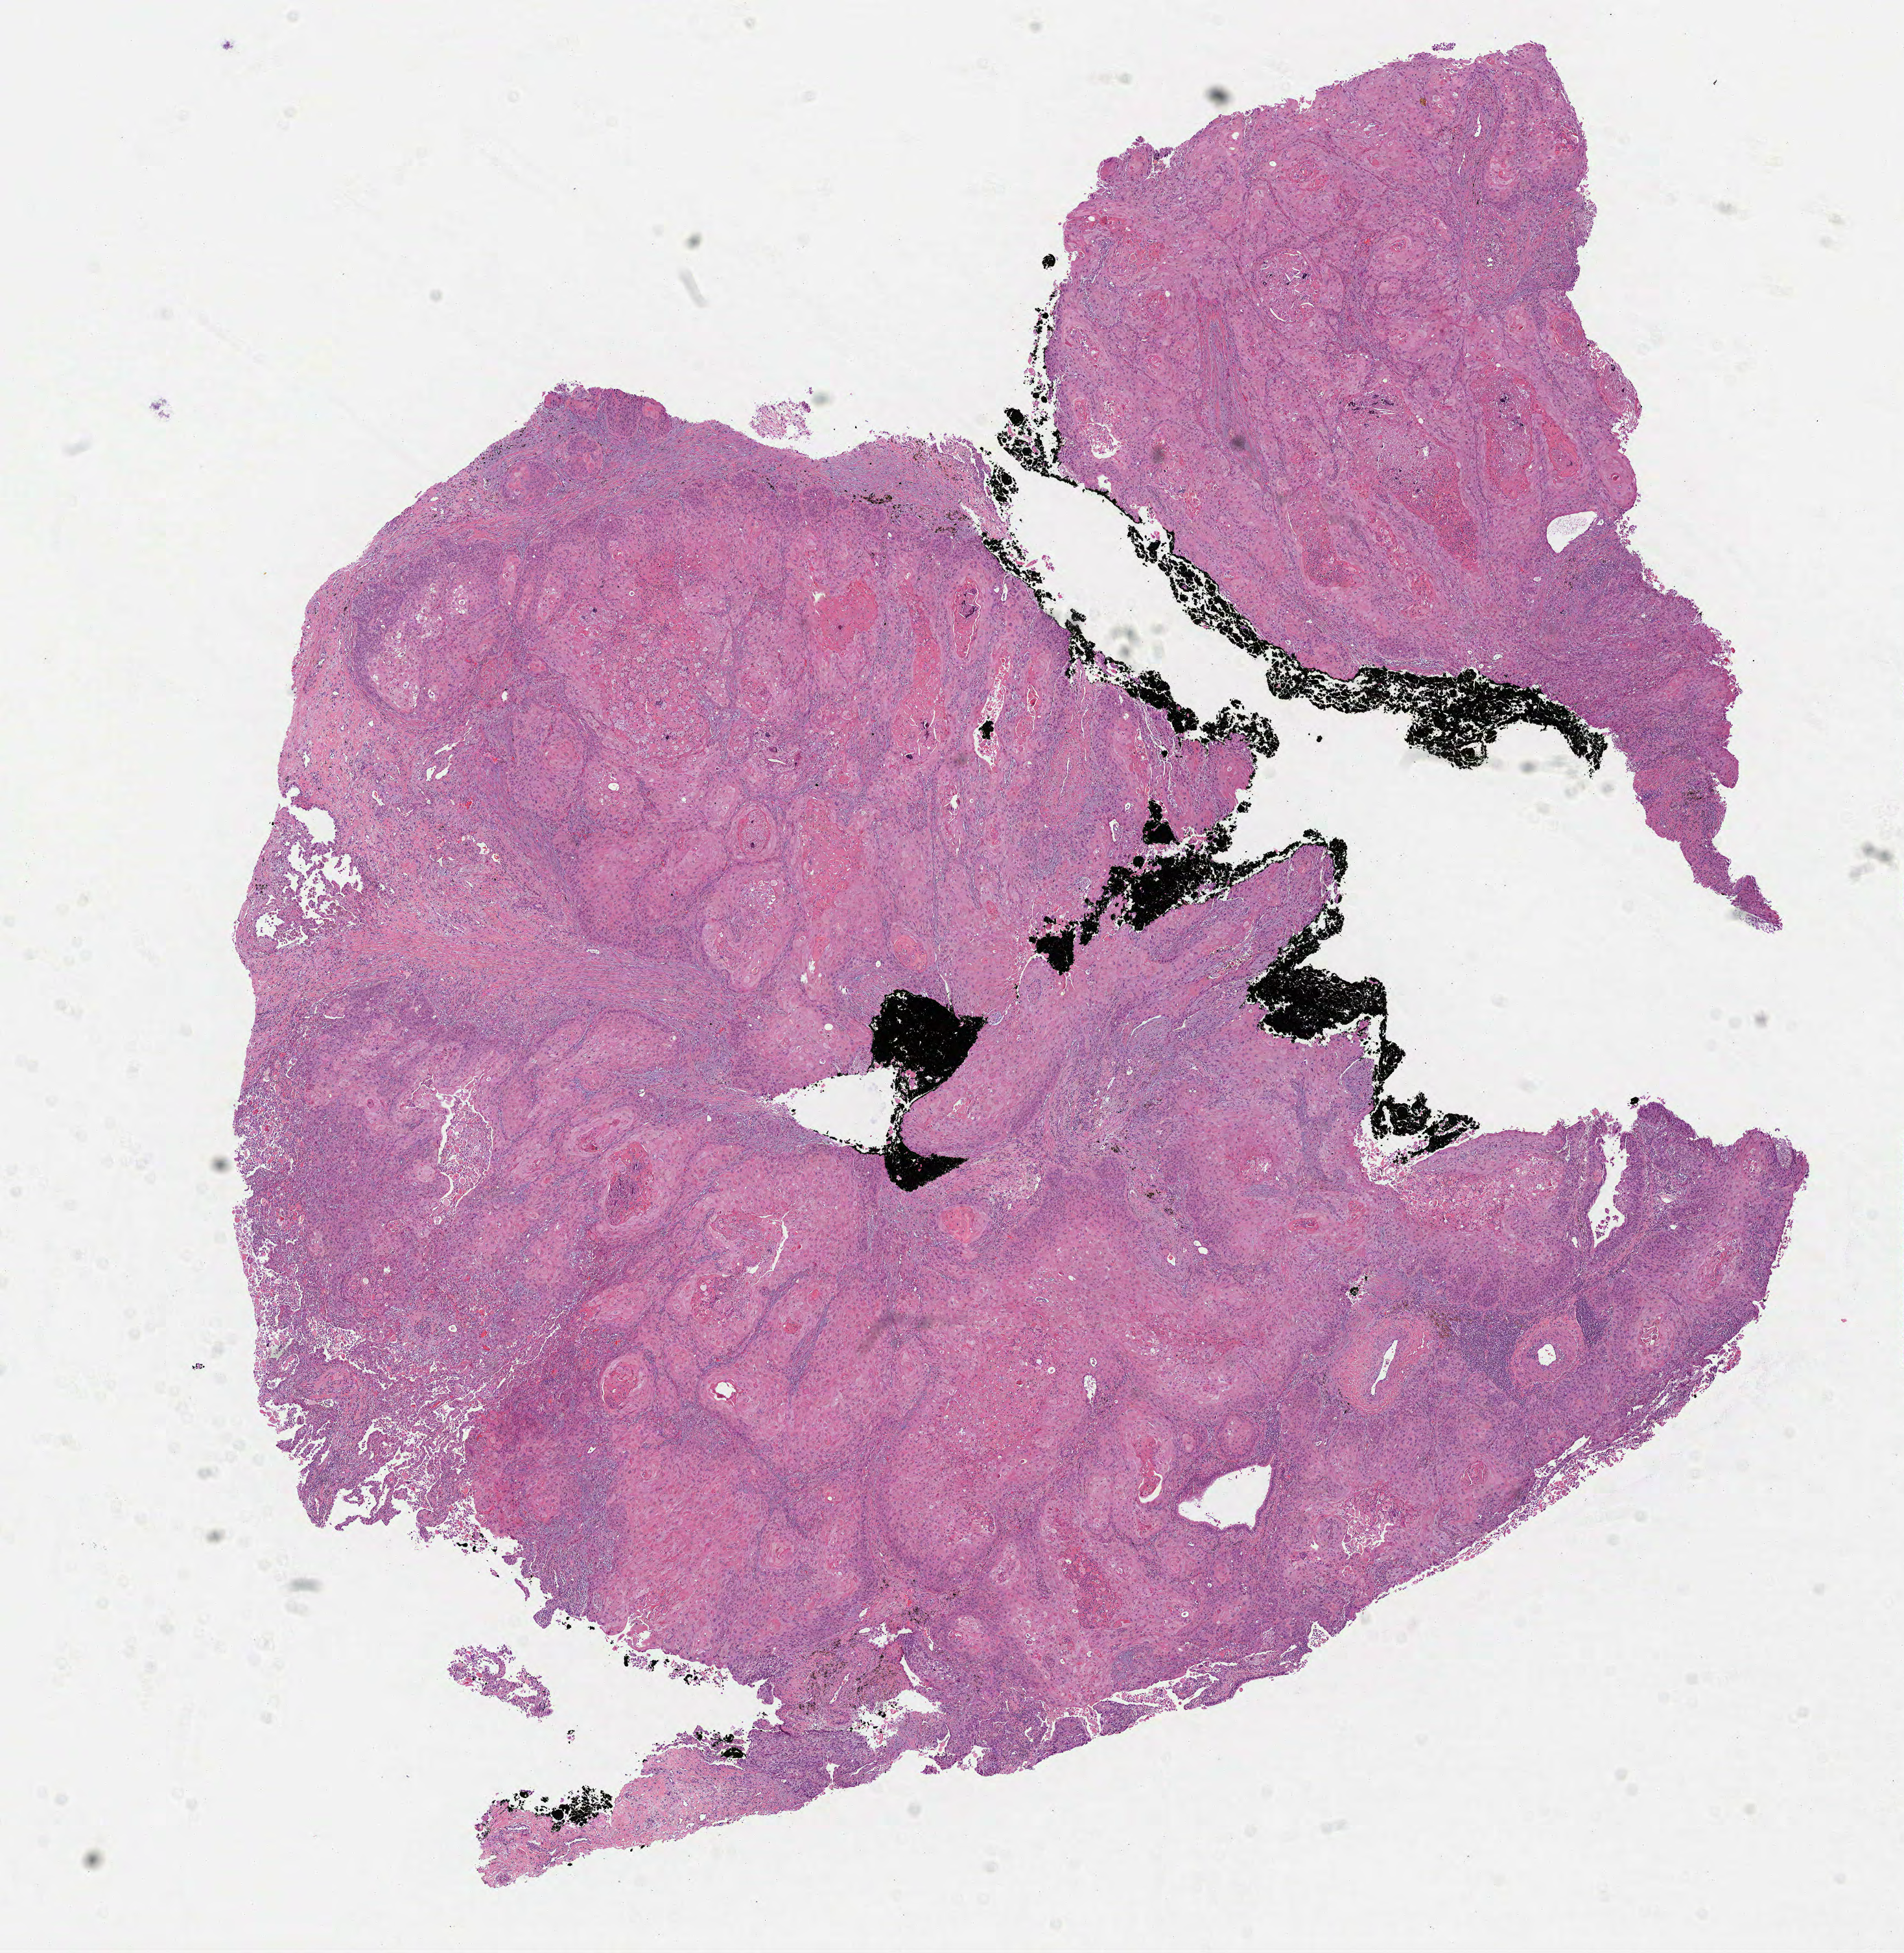
Digitized H&E-stained tissue section (whole slide), shown as a low-resolution overview of the whole scanned area (about 11.8 x 12.2 mm, from a 40x scan), formalin-fixed paraffin-embedded (FFPE) diagnostic section, sample: primary tumour, lung. Male patient; age at initial diagnosis 75 years.
Histologic diagnosis: Squamous cell carcinoma, NOS (upper lobe, lung). AJCC pathologic stage: IIB. Laterality: right.